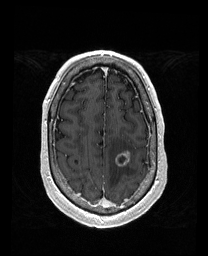
Brain MRI from a brain-tumour surgery series, one axial slice; slice 140 of 192 in the series (ordered by position); T1-weighted post-contrast; 1 mm slice thickness; 208 × 256 image matrix, field of view 211 × 260 mm. Case-level facts recorded for this patient, not image findings: histopathology: Metastatic Carcinoma from Lung Adenocarcinoma; tumour location: Left Frontal.
Annotated regions visible in this slice (outlined manually by an expert reader):
- tumour: bounding box [x1, y1, x2, y2] px = [115, 152, 129, 166]